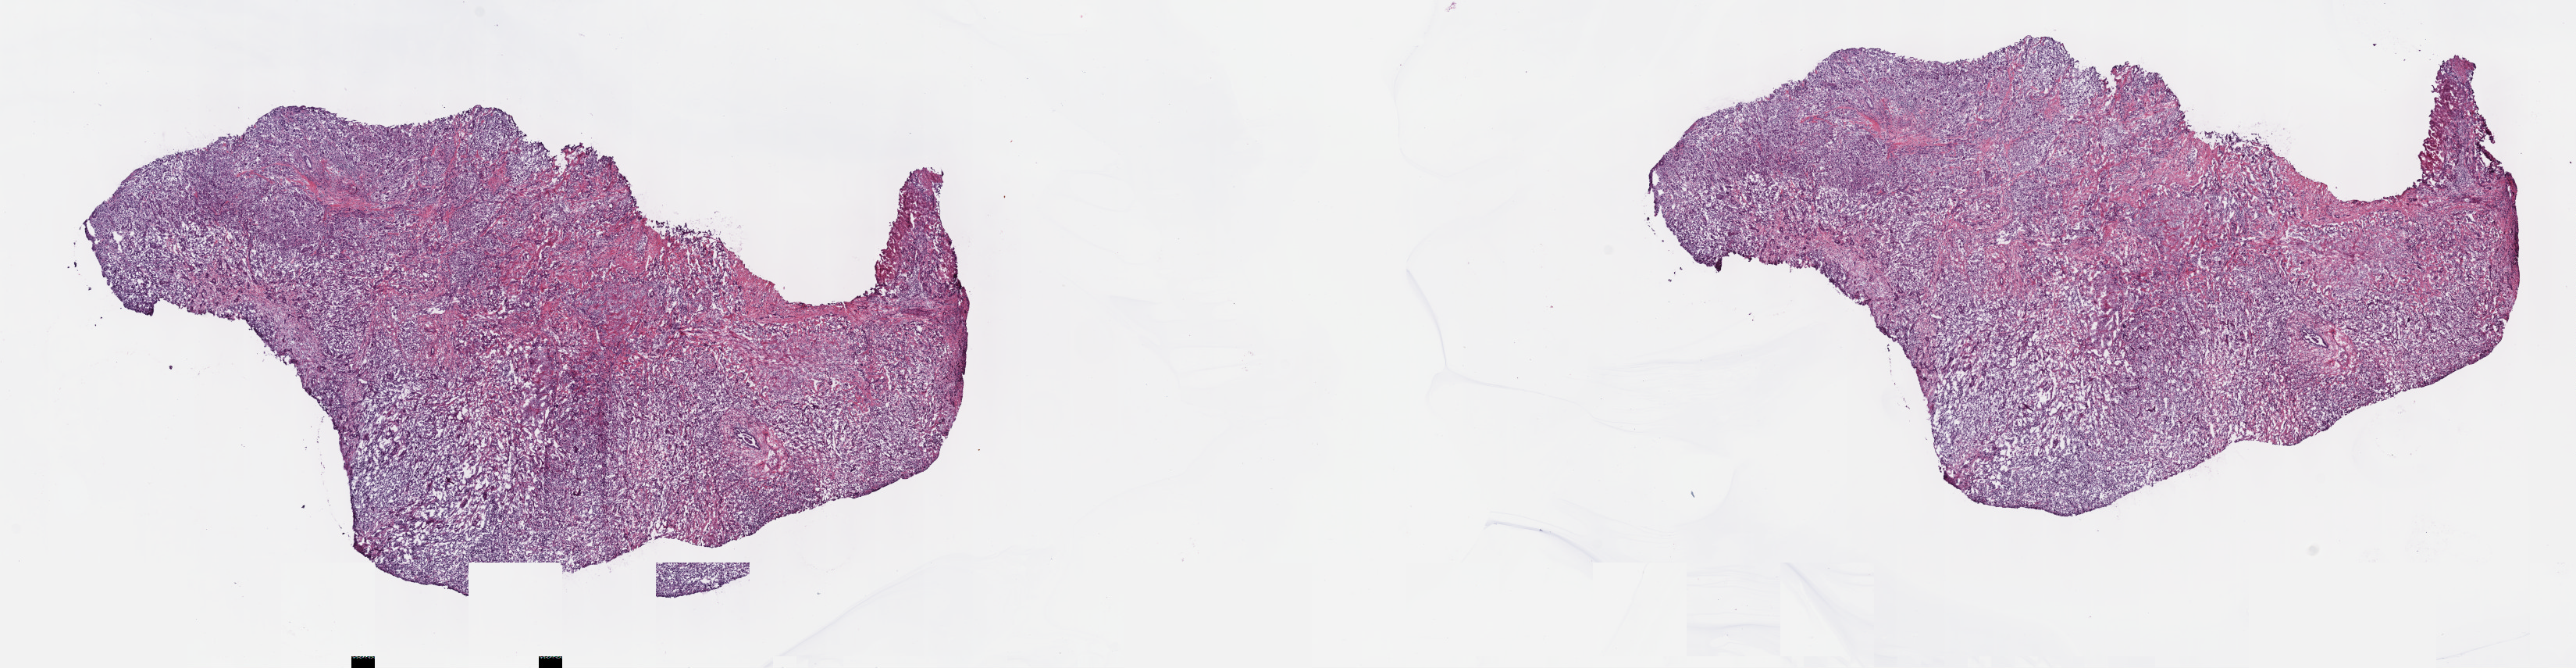
H&E-stained whole-slide image — low-resolution overview of the scanned area, about 26.7 x 6.9 mm. Frozen section from the top of the tissue portion. Sample: primary tumour, bile duct. Male patient; age at initial diagnosis 52 years. Histologic grade: G3 (poorly differentiated). Composition of this section per pathologist review: tumour cells 50%, tumour nuclei 60%, normal cells 0%, stromal cells 50%, necrosis 0%. Inflammatory infiltration, as recorded: lymphocyte infiltration 80%, monocyte infiltration 20%, neutrophil infiltration 0%.
TNM: T1 NX MX. AJCC pathologic stage: I (7th edition). Diagnosis: Cholangiocarcinoma (intrahepatic bile duct).